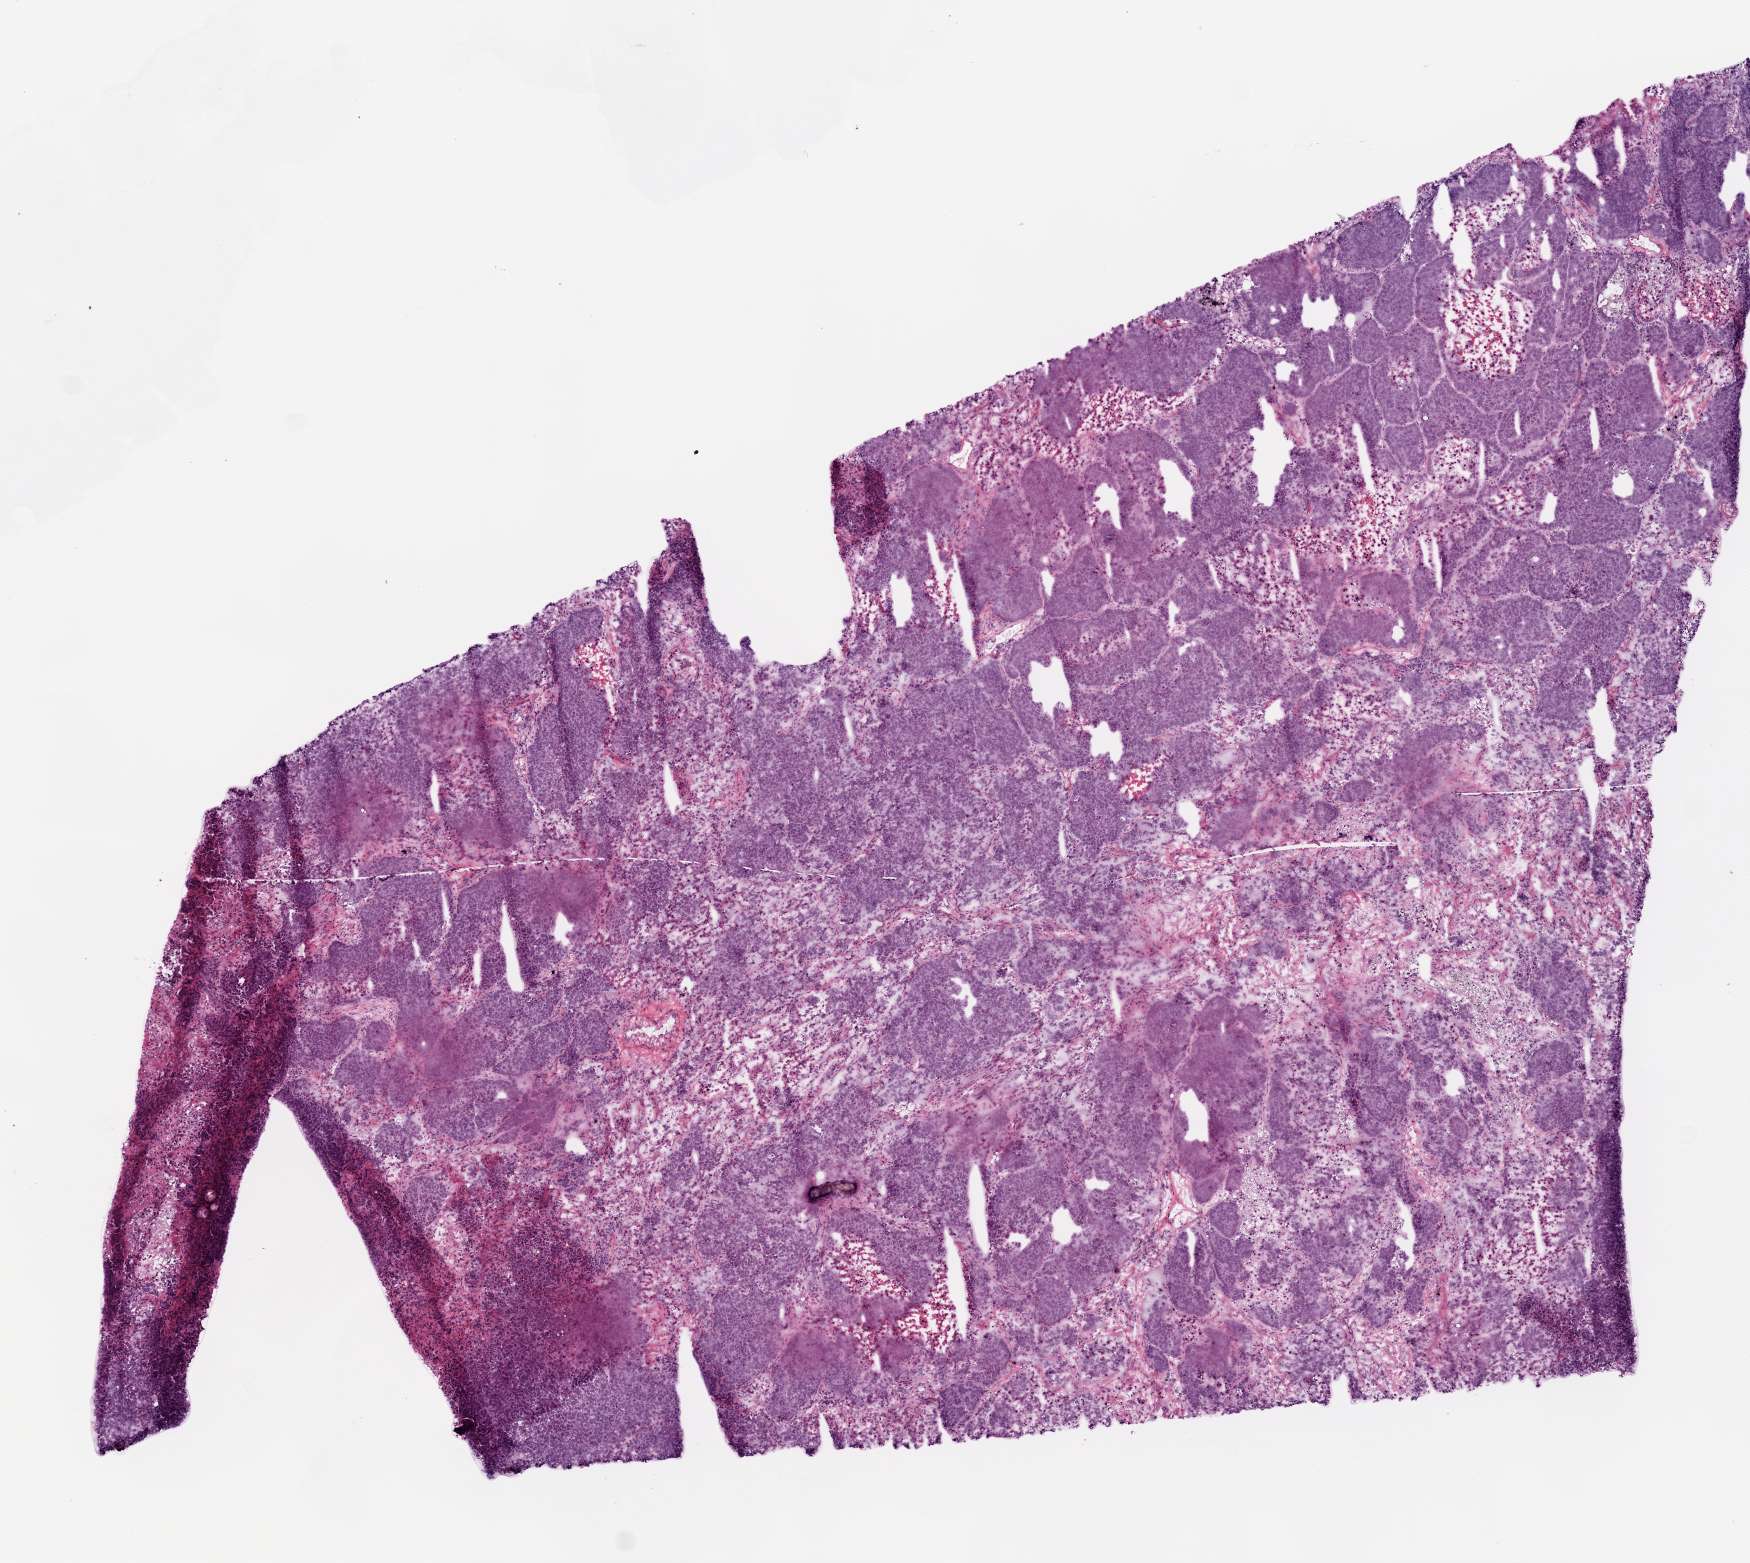
Digitized Hematoxylin and eosin (H&E) stained tissue section (whole slide), whole scanned area (about 7.0 x 6.3 mm, from a 20x scan) shown as a low-resolution overview. Frozen section from the top of the tissue portion. Primary tumour sample from the lung. Male, age 66 years at initial diagnosis.
Histologic diagnosis: Squamous cell carcinoma, NOS (upper lobe, lung).